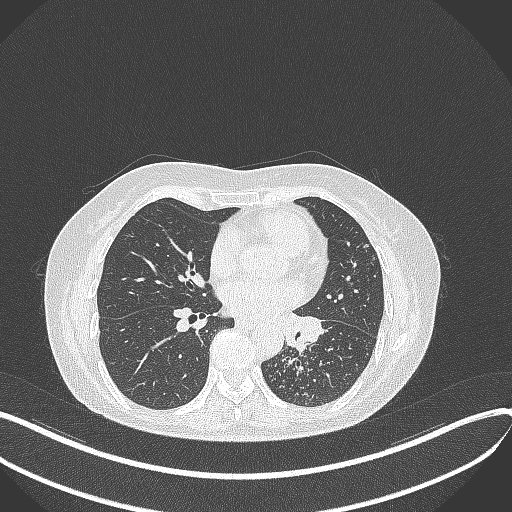
Chest CT, one axial slice; position 193 of 429 along the scan axis; reconstruction kernel B70f; lung window (W 1500 / L -600 HU); 512 × 512 image matrix, field of view 400 × 400 mm. Female patient, age 63 years. From the clinical record (not read from this slice): clinical TNM (as recorded): T1b N0 M0.
Structures marked on this image (rectangle marked by the reading radiologist):
- lung tumour (recorded histology: adenocarcinoma): box from (x=276, y=305) to (x=327, y=352) px